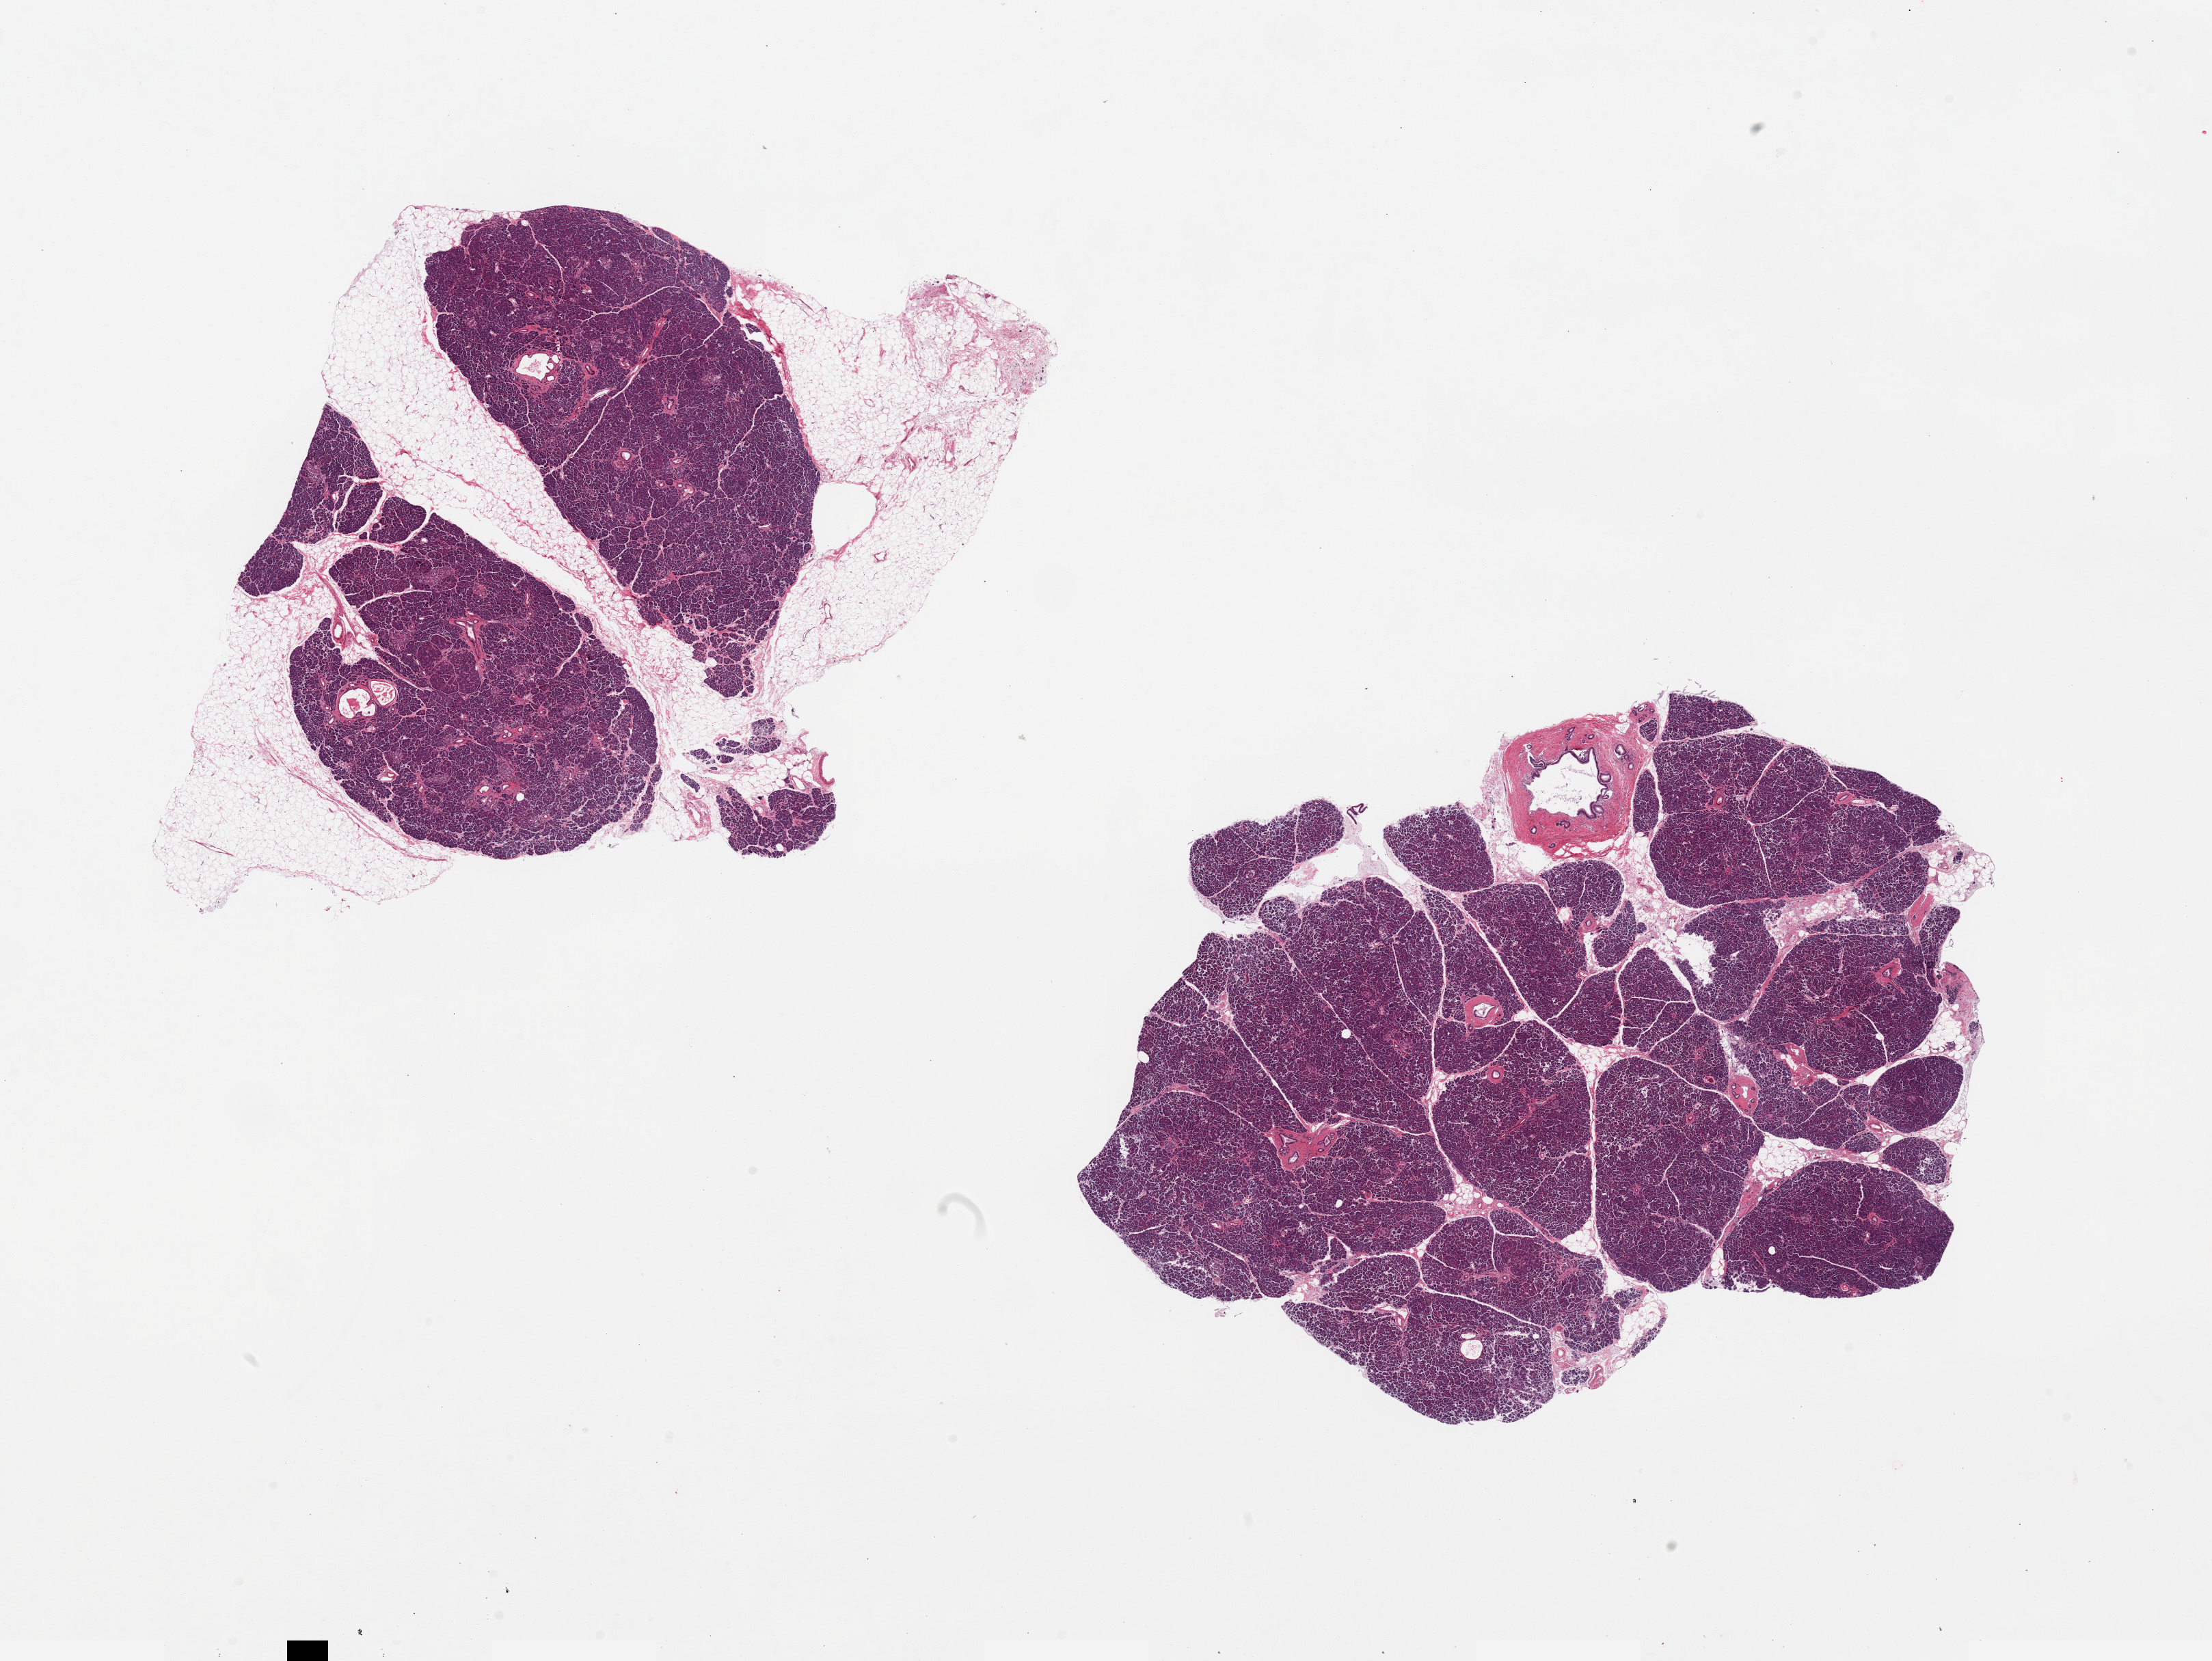
Hematoxylin and eosin (H&E) whole-slide image, whole scanned area (about 25.6 x 19.2 mm) shown as a low-resolution overview; PAXgene-fixed paraffin-embedded (PFPE) section; target tissue: pancreas; donor tissue sample. Donor: male.
Pathologist's review note for this sample: 2 pieces, 9.5x8 and 12x8mm; adherent fatty nubbins on one ~2mm; Moderate saponification; occasonal Islets visible.